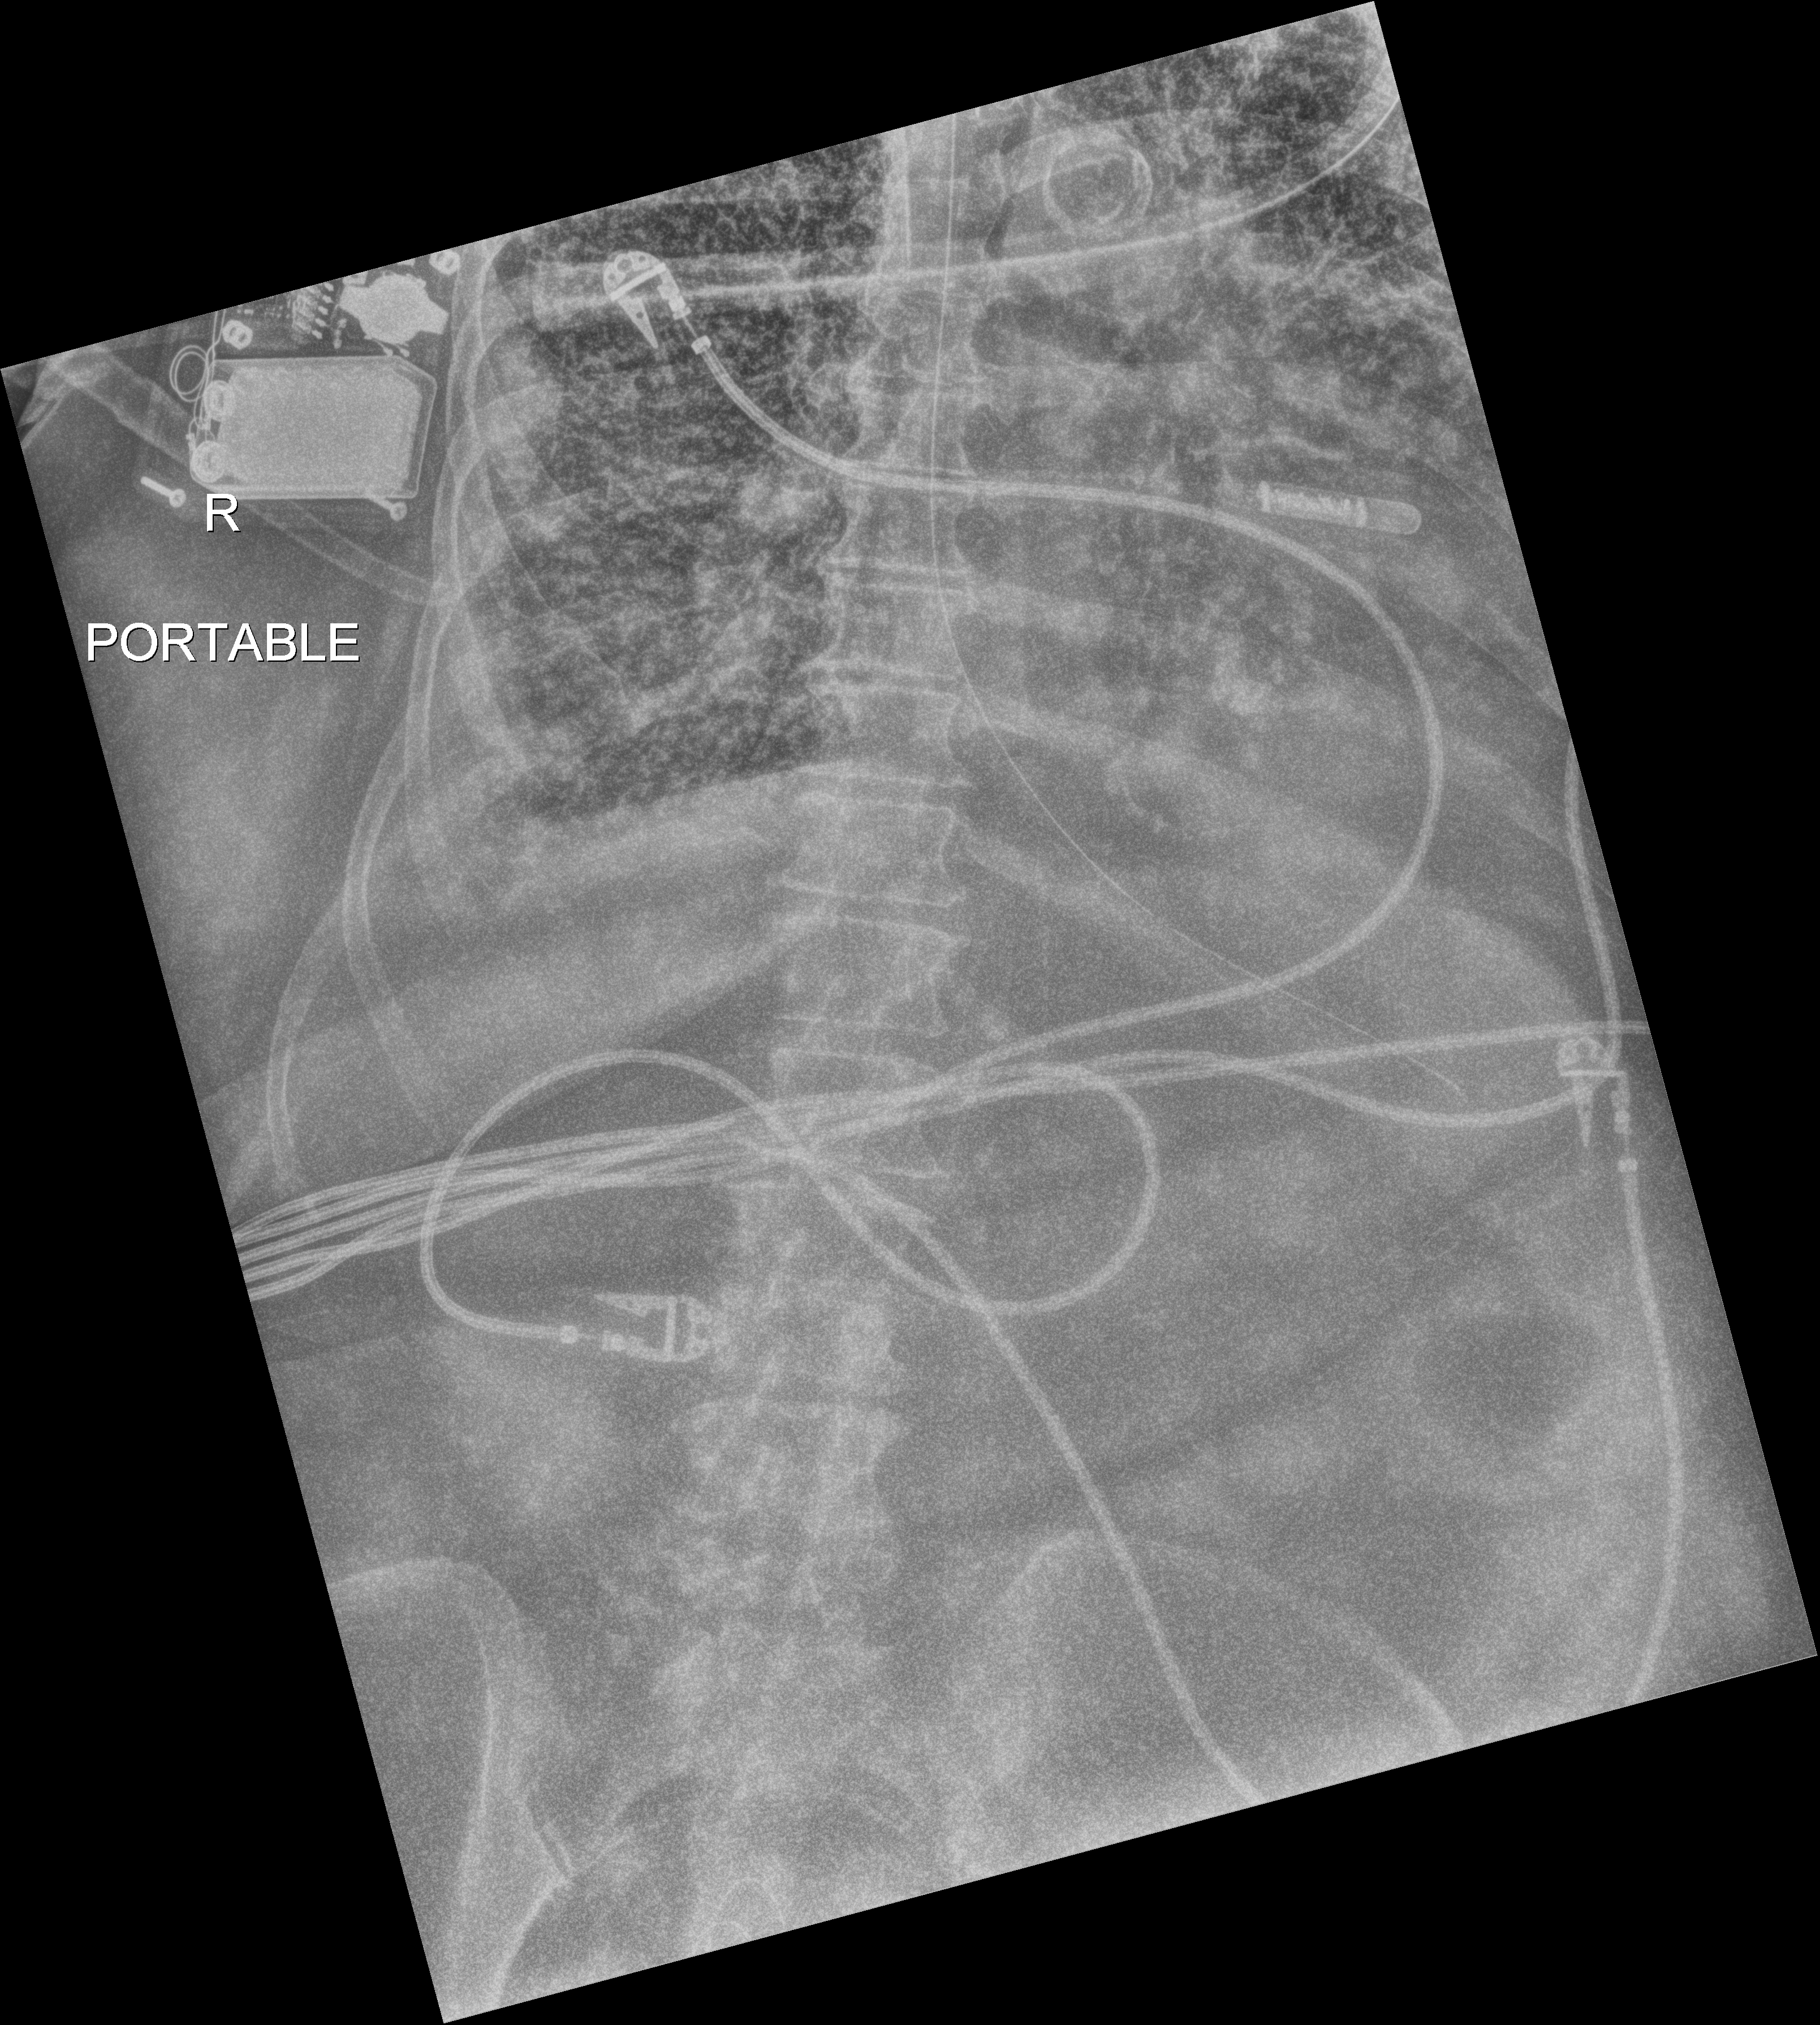
Bedside chest radiograph (digital radiography); anteroposterior (AP) projection. Patient hospitalised with COVID-19; female, aged 60–74 years.
From the hospital-stay record, not from the radiograph (when in the stay this image was taken is not recorded):
- mechanically ventilated during this hospital stay: yes